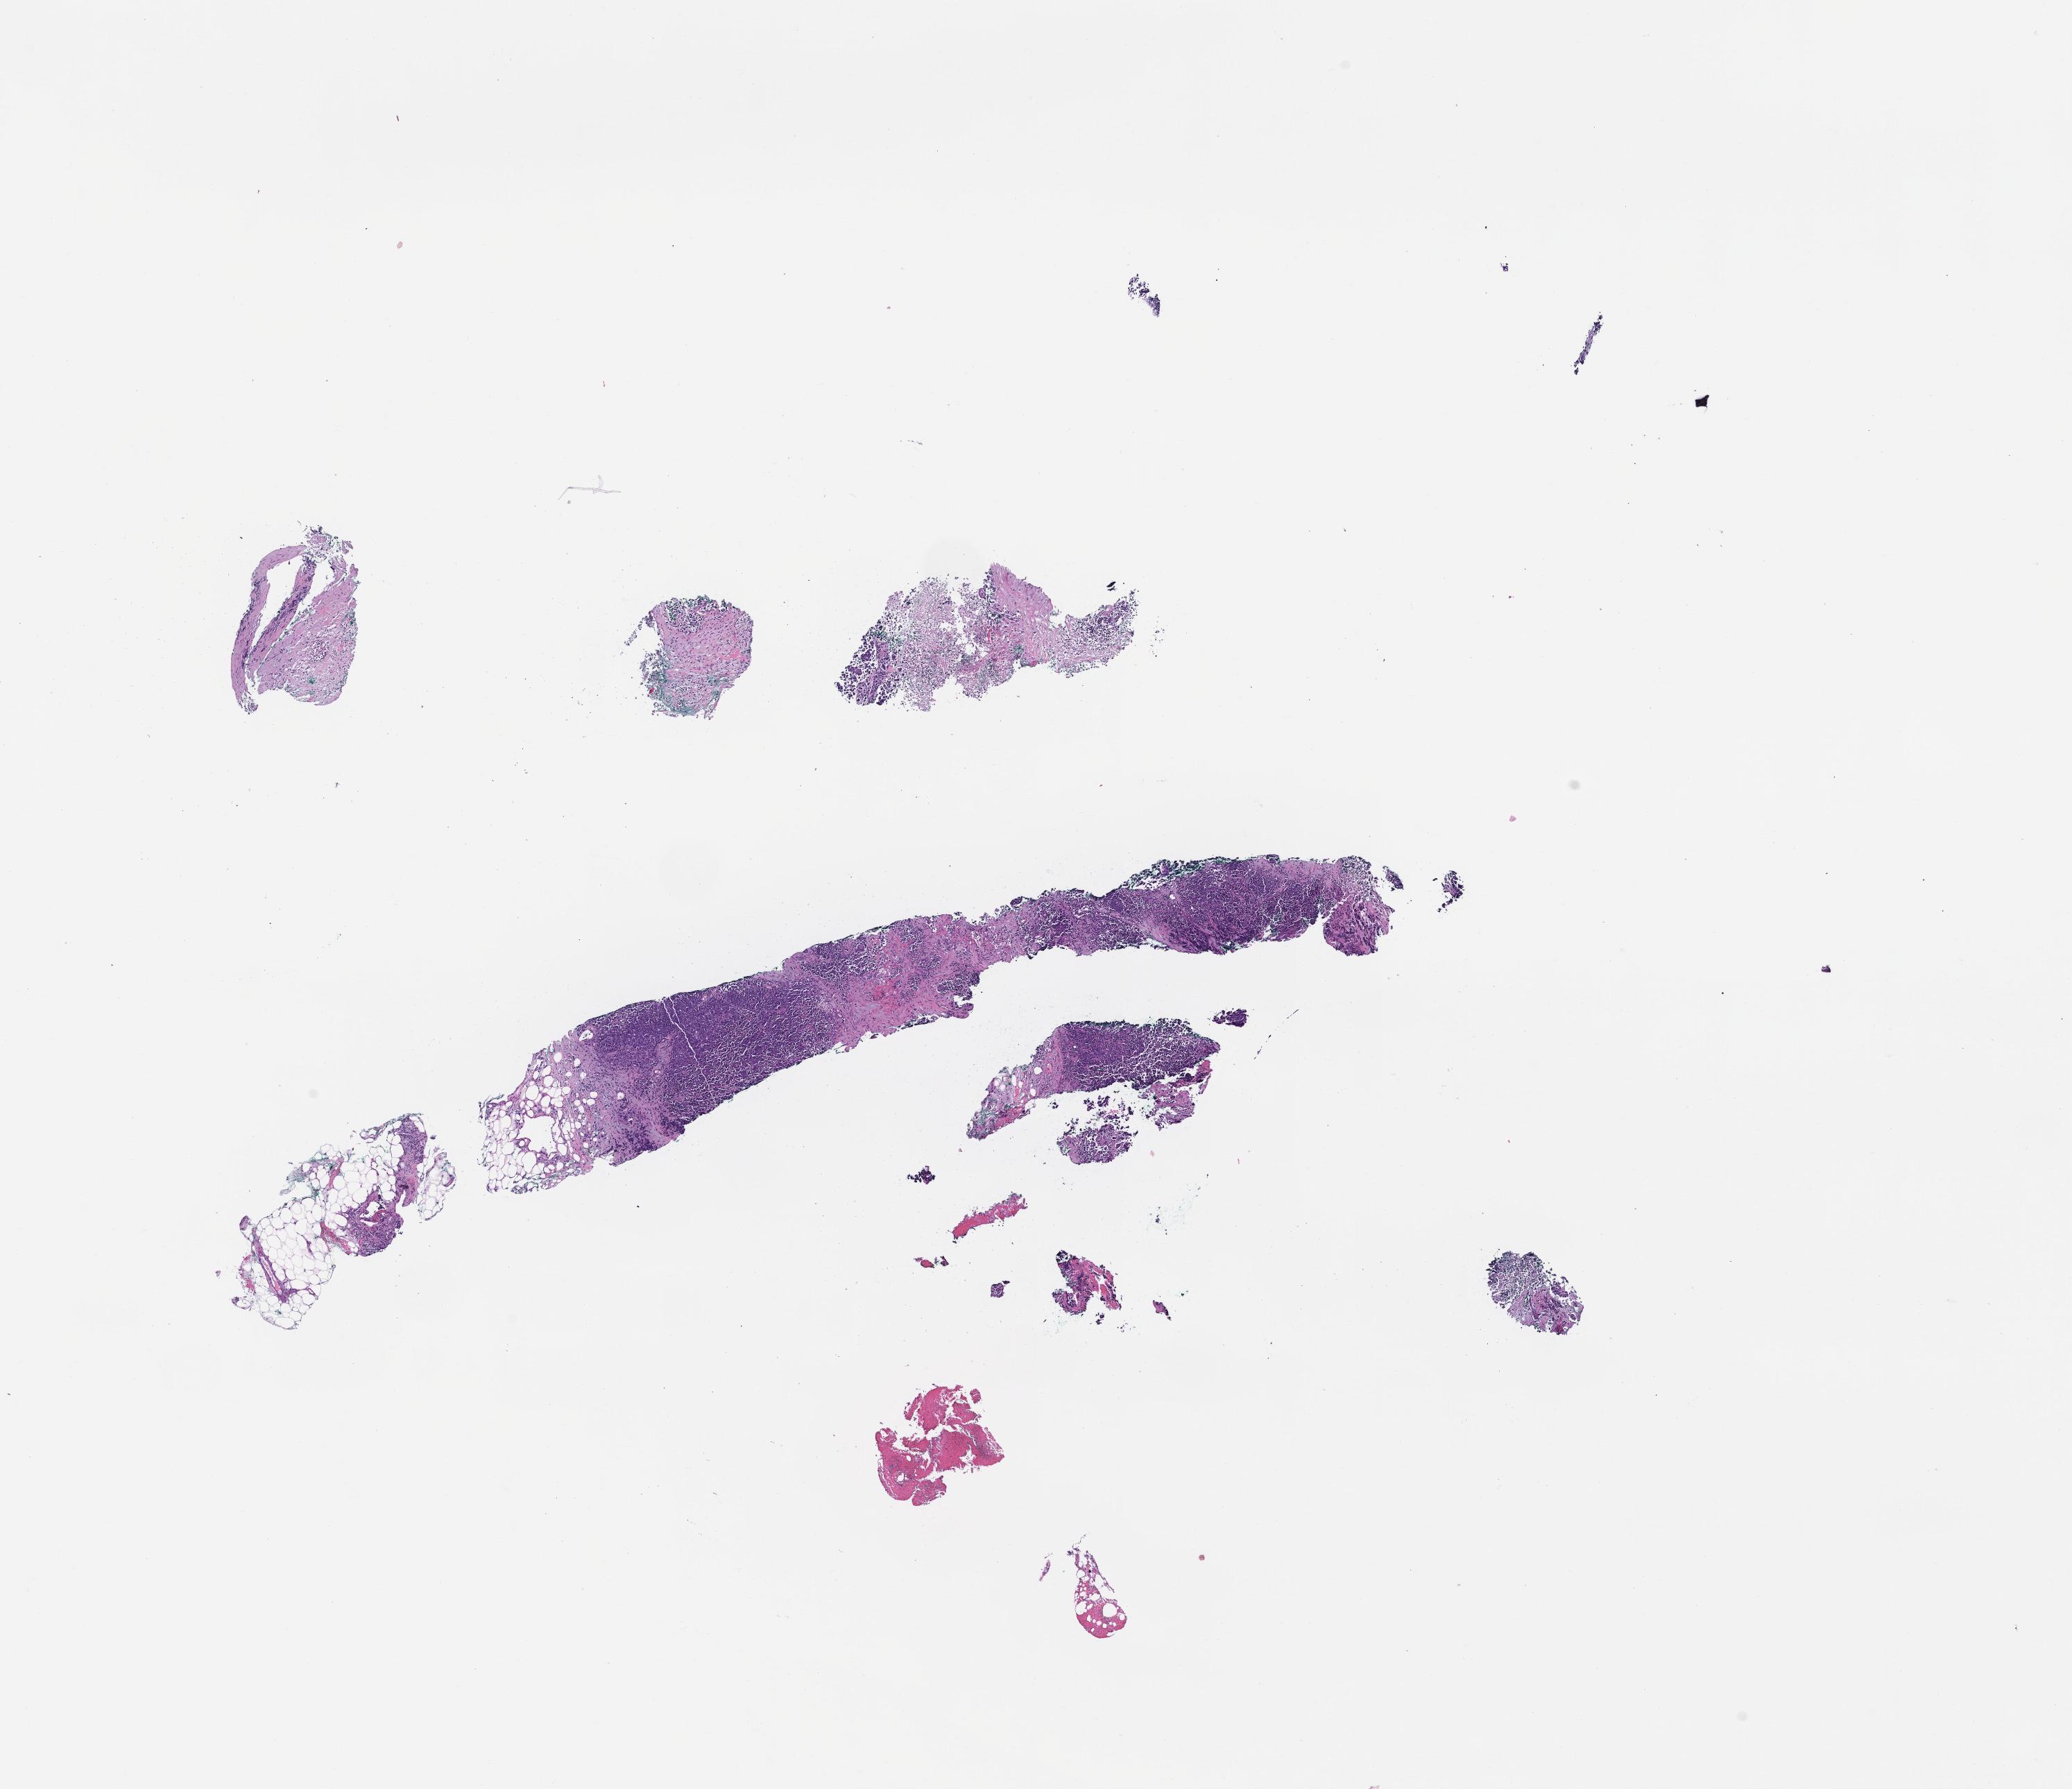
Hematoxylin and eosin (H&E) whole-slide image — low-resolution overview of the scanned area, about 12.1 x 10.4 mm. Formalin-fixed, paraffin-embedded (FFPE) tissue. Patient: male.
• this section: metastatic tumor tissue
• primary diagnosis of the patient: Non-Small Cell Lung Carcinoma